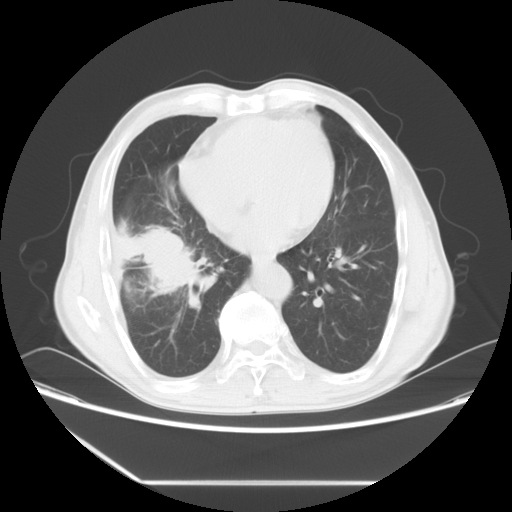
Chest CT, one axial slice. Slice 24 of 60 in the series (ordered by position). Reconstruction kernel STANDARD. Lung window (W 1500 / L -600 HU). 5 mm slice thickness. 512 × 512 image matrix. Male patient, age 72 years. Case-level facts recorded for this patient, not image findings: clinical TNM (as recorded): T1c N0 M0.
Annotated regions visible in this slice (bounding box drawn by a radiologist):
- lung tumour (recorded histology: squamous cell carcinoma): bounding box (x1, y1, x2, y2) in pixels: (113, 215, 194, 303)